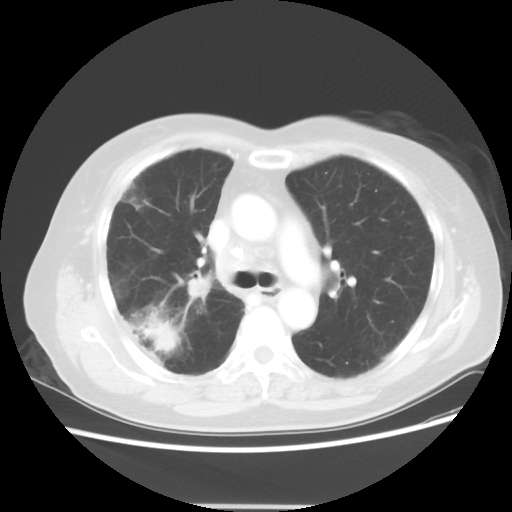
Chest CT, one axial slice. Slice 31 of 50 in the series (ordered by position). Reconstruction kernel STANDARD. Lung window (W 1500 / L -600 HU). 5 mm slice thickness. 512 × 512 image matrix, field of view 360 × 360 mm. Patient: female, 72 years. Case-level facts recorded for this patient, not image findings: clinical TNM (as recorded): T2 N1 M0.
Annotated regions visible in this slice (rectangle marked by the reading radiologist):
- lung tumour (recorded histology: adenocarcinoma): box from (x=144, y=318) to (x=177, y=352) px